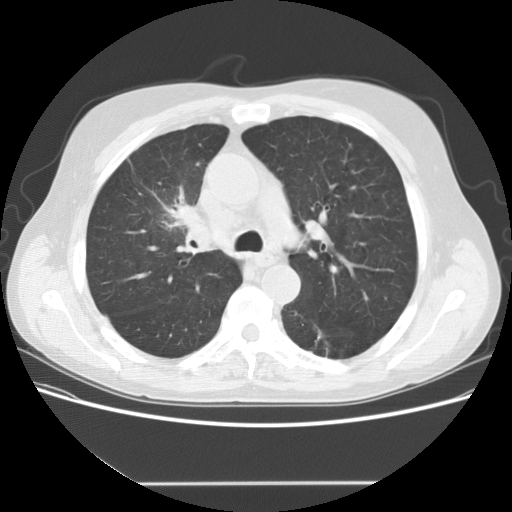
Low-dose screening chest CT, one axial slice. Position 104 of 153 along the scan axis. Reconstruction kernel STANDARD. 120 kVp. Lung window (W 1500 / L -600 HU). 2.5 mm slice thickness. 512 × 512 image matrix, field of view 360 × 360 mm.
Structures marked on this image (manually delineated by an expert):
- lesion 1 (tumor, upper lobe of right lung): bounding box [x1, y1, x2, y2] px = [168, 204, 200, 225]